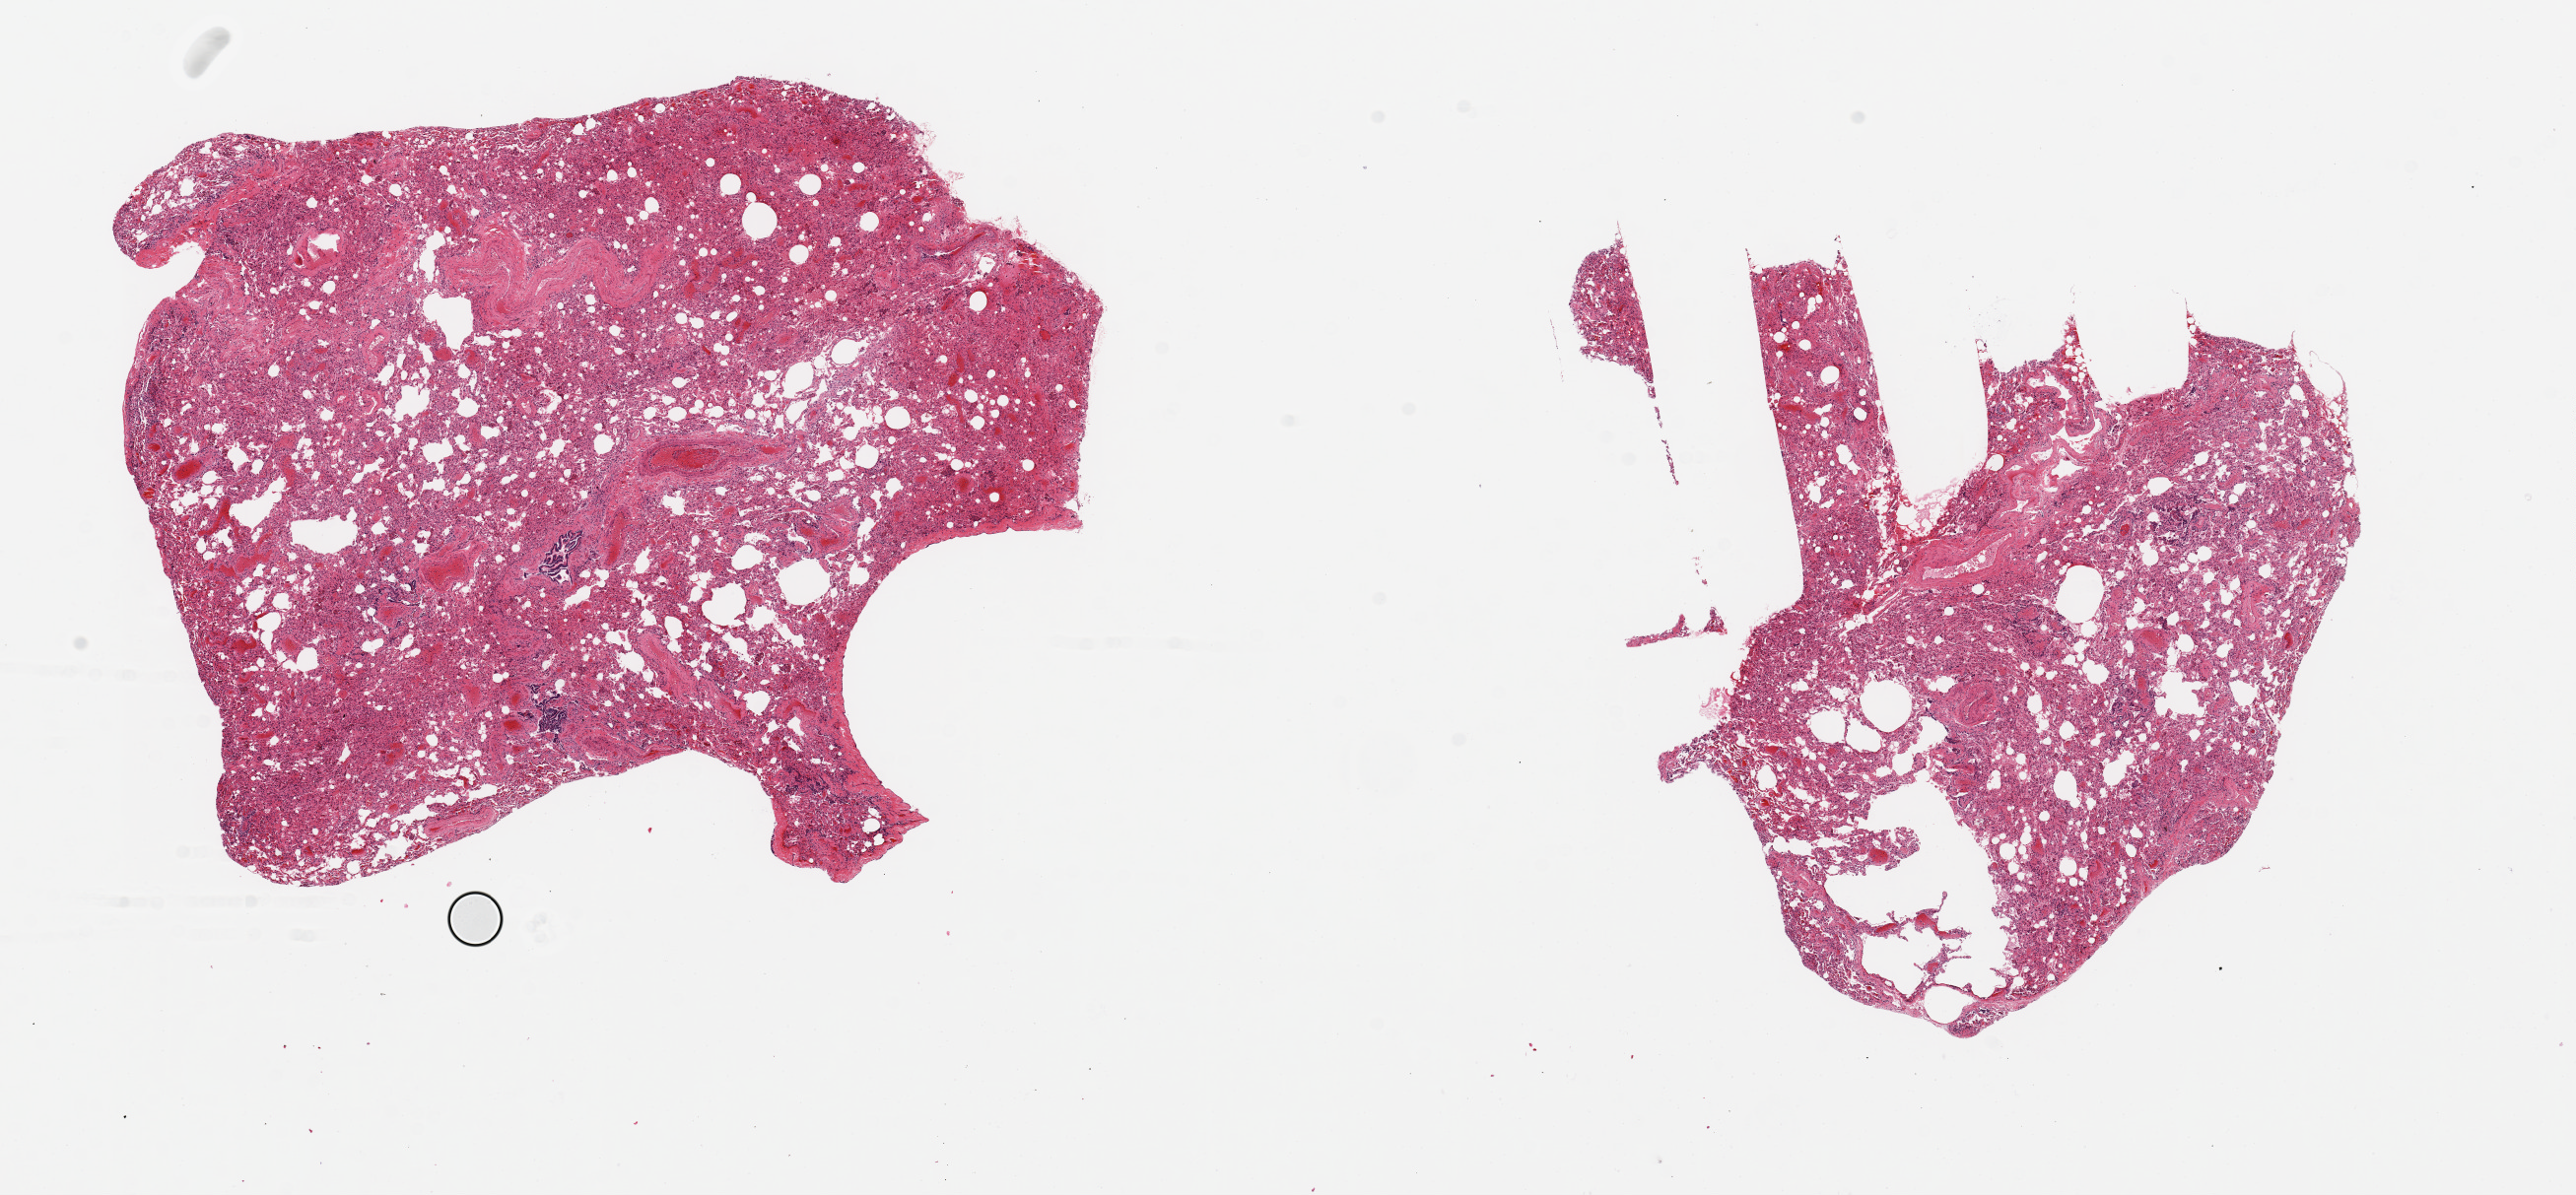
H&E whole-slide image — low-resolution overview of the scanned area, about 20.7 x 9.6 mm. PAXgene-fixed paraffin-embedded (PFPE) section. Sampled site (target tissue): lung. Tissue donor sample. Donor sex: male.
Reviewer comment on this tissue sample: 2 pieces 8x7 & 7x6mm; moderate congestion/atalectasis.